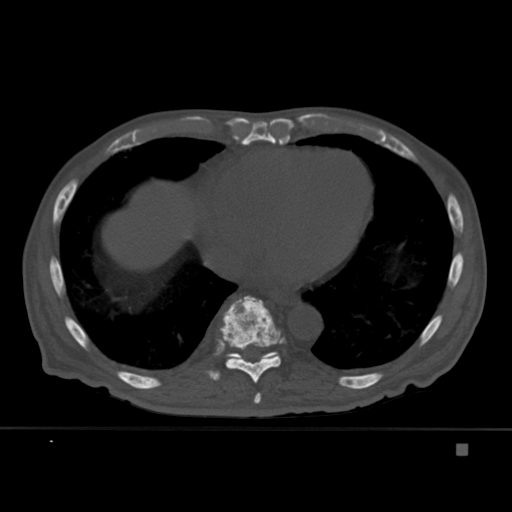
CT including the spine, one axial slice; position 245 of 451 along the scan axis; bone window (W 1800 / L 400 HU); 1.5 mm slice thickness; 512 × 512 image matrix. Male patient, age 75 years. Case-level facts recorded for this patient, not image findings: primary cancer: prostate.
Annotated regions visible in this slice (semi-automatically segmented with operator editing):
- T10 vertebra: bounding box <226,352,279,358> (left, top, right, bottom; pixels)
- T8 vertebra: <254,392,261,404>
- T9 vertebra: <207,295,286,383>